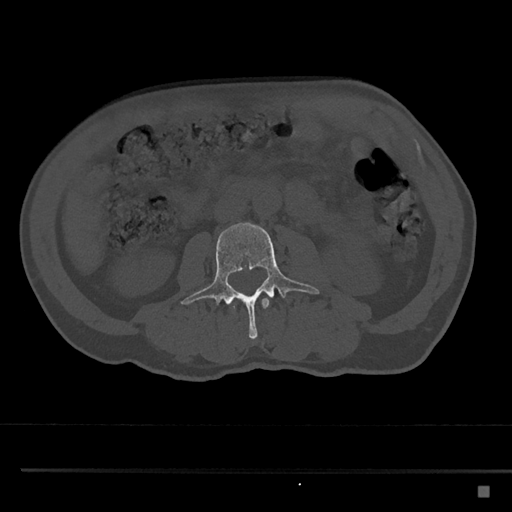
CT including the spine, one axial slice; position 702 of 797 along the scan axis; reconstruction kernel Br40s/3; 120 kVp; bone window (W 1800 / L 400 HU); 0.5 mm slice thickness; 512 × 512 image matrix. Patient: male, 59 years. Case-level facts recorded for this patient, not image findings: primary cancer: prostate.
Outlined on this slice (semi-automatic segmentation, software-assisted and operator-edited):
- L2 vertebra: bounding box <262,298,269,308> (left, top, right, bottom; pixels)
- L3 vertebra: <181,222,320,341>